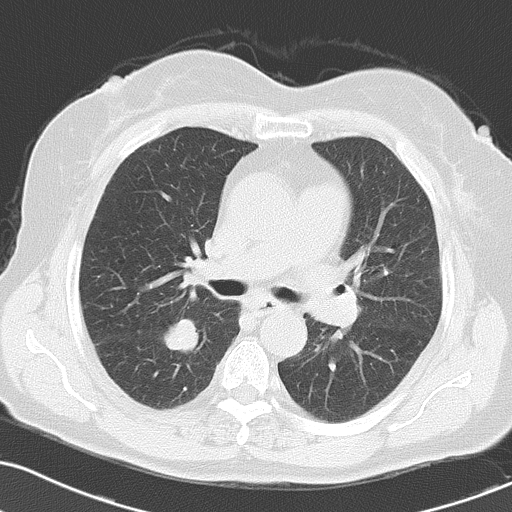
Chest CT, one axial slice; position 35 of 55 along the scan axis; 120 kVp; lung window (W 1500 / L -600 HU); 5 mm slice thickness; 512 × 512 image matrix. Patient: female, 70 years. Case-level facts recorded for this patient, not image findings: clinical TNM (as recorded): T1c N3 M0.
Outlined on this slice (bounding box drawn by a radiologist):
- lung tumour (recorded histology: small cell carcinoma): bounding box <157,308,201,360> (left, top, right, bottom; pixels)